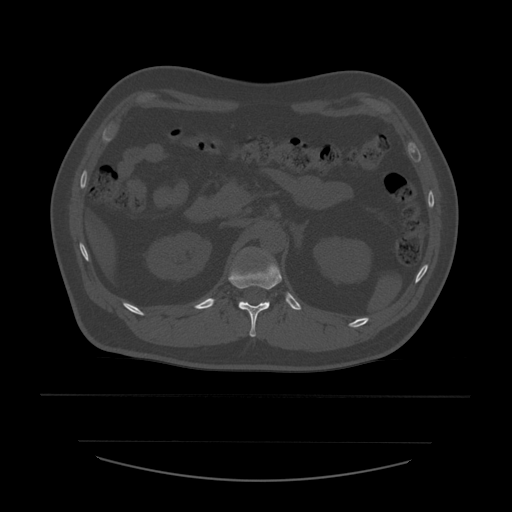
CT including the spine, one axial slice; position 245 of 532 along the scan axis; reconstruction kernel STANDARD; bone window (W 1800 / L 400 HU); 1.25 mm slice thickness; 512 × 512 image matrix, field of view 441 × 441 mm. Patient age 44 years. Case-level facts recorded for this patient, not image findings: primary cancer: soft tissue sarcoma.
Outlined on this slice (semi-automatically segmented with operator editing):
- L1 vertebra: bounding box [x1, y1, x2, y2] px = [239, 301, 242, 304]
- T12 vertebra: [229, 254, 282, 337]